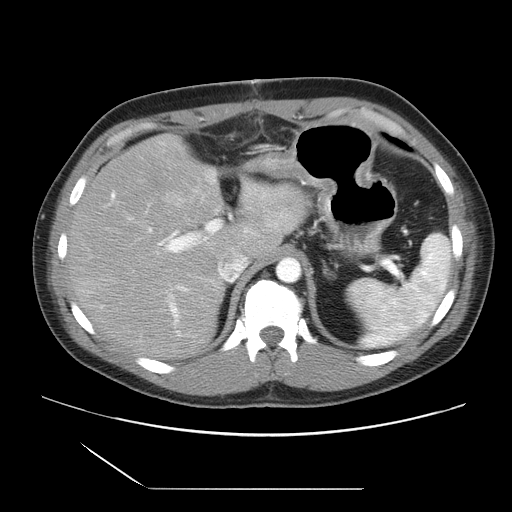
Contrast-enhanced abdominal CT, one axial slice; slice 19 of 39 in the series (ordered by position); 120 kVp; soft-tissue window (W 400 / L 40 HU); 5 mm slice thickness; 512 × 512 image matrix, field of view 395 × 395 mm. Male patient, age 39 years. From the clinical record (not read from this slice): diagnosis: colorectal cancer liver metastases, imaged before liver resection; multiple liver metastases: yes; largest metastasis: 1.3 cm; disease in both lobes: no.
Structures marked on this image (outlined manually by an expert reader):
- hepatic veins: bounding box (x1, y1, x2, y2) in pixels: (164, 255, 247, 308)
- liver: (66, 136, 307, 360)
- planned liver remnant (the part of the liver to remain after resection): (118, 136, 307, 259)
- portal vein (with intrahepatic branches): (99, 190, 220, 328)